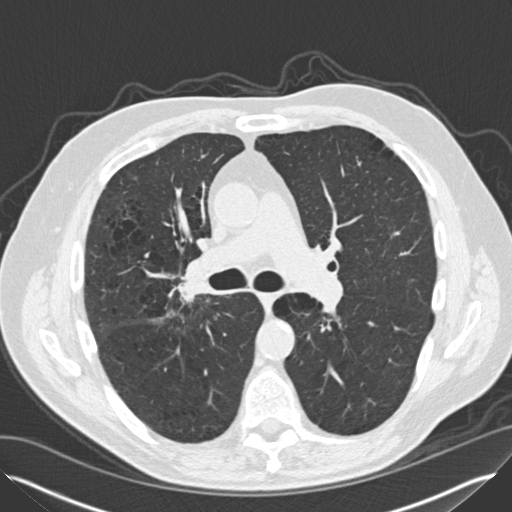
Low-dose screening chest CT, one axial slice. Slice 86 of 149 in the series (ordered by position). 120 kVp. Lung window (W 1500 / L -600 HU). 512 × 512 image matrix, field of view 370 × 370 mm.
Annotated regions visible in this slice (expert manual segmentation):
- lesion 2 (tumor, hilum of right lung): box from (x=185, y=259) to (x=208, y=296) px